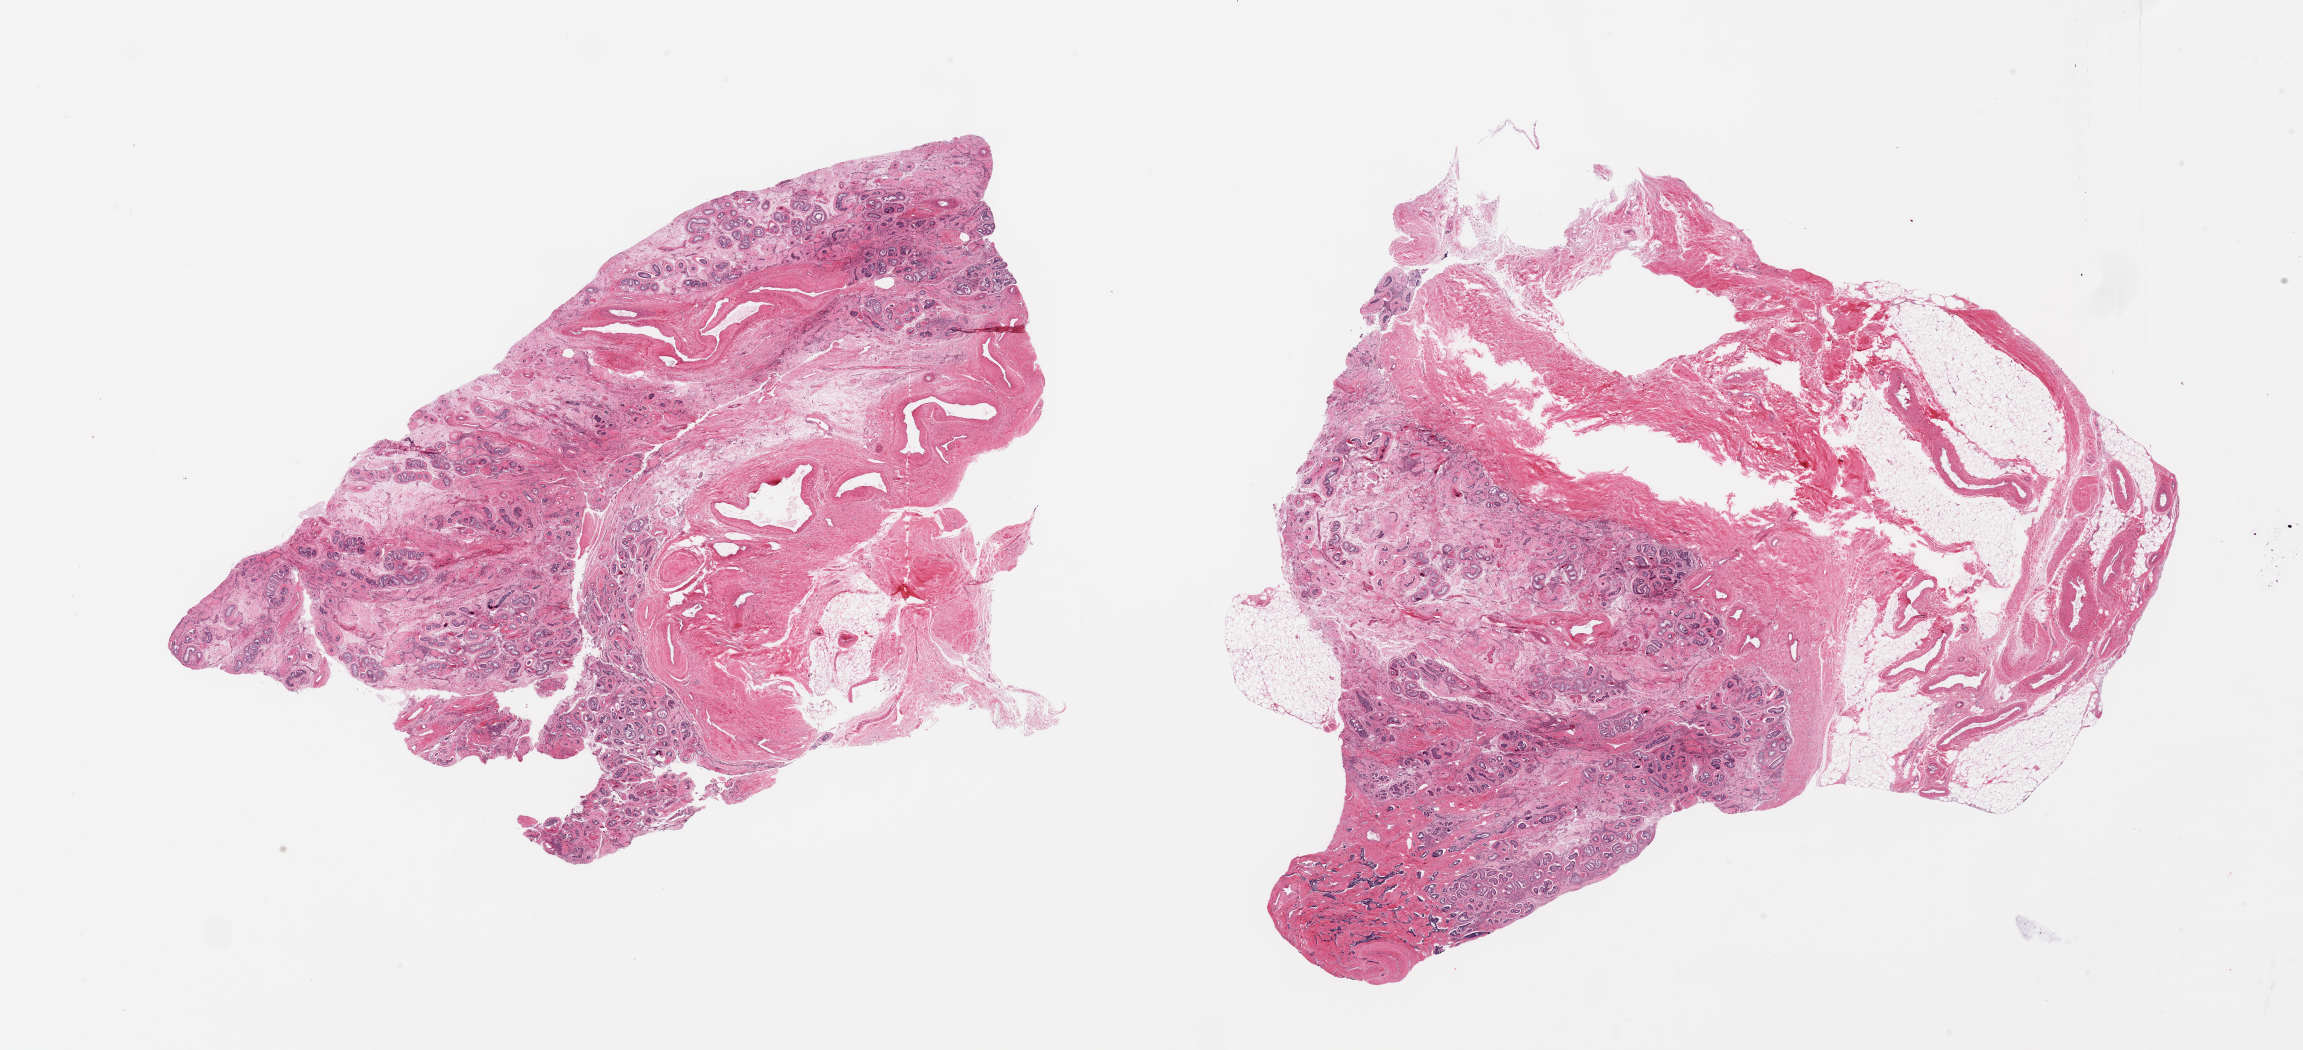
Haematoxylin and eosin whole-slide image, brightfield — shown as a low-resolution overview of the whole scanned area (about 36.4 x 16.6 mm, acquisition: 20x scan). PAXgene-fixed paraffin-embedded (PFPE) section. Section of testis (target tissue). Donor tissue sample. Donor: male.
- pathologist's review note for this sample: 2 pieces; diffuse tubular hyalinization with plentiful residual Leydig cells, consistent with Klinefelter syndrome; includes significant contaminating component of fat/vessels and rete testis